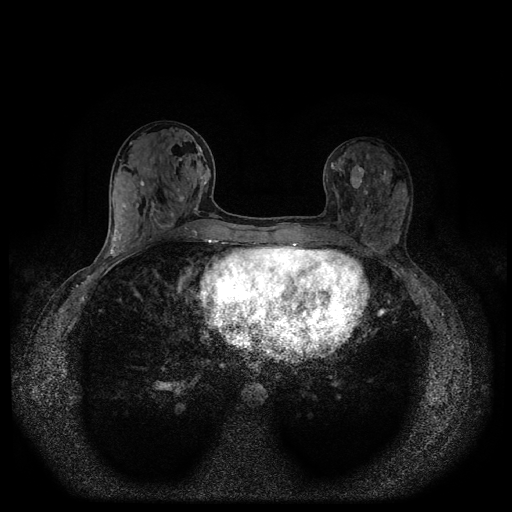
Breast MRI (dynamic contrast-enhanced, multi-phase), one axial slice; slice 40 of 116 in the series (ordered by position); dynamic contrast-enhanced series, time point 2 of 5 at this slice position (early post-contrast); 1.5 T; TE 2.6 ms, TR 5.4 ms; 2 mm slice thickness; 512 × 512 image matrix, field of view 340 × 340 mm. Female patient, age 32 years.
Outlined on this slice (semi-automatic segmentation, software-assisted and operator-edited):
- breast lesion (labelled benign in the annotation): bounding box (x1, y1, x2, y2) in pixels: (349, 165, 365, 189)